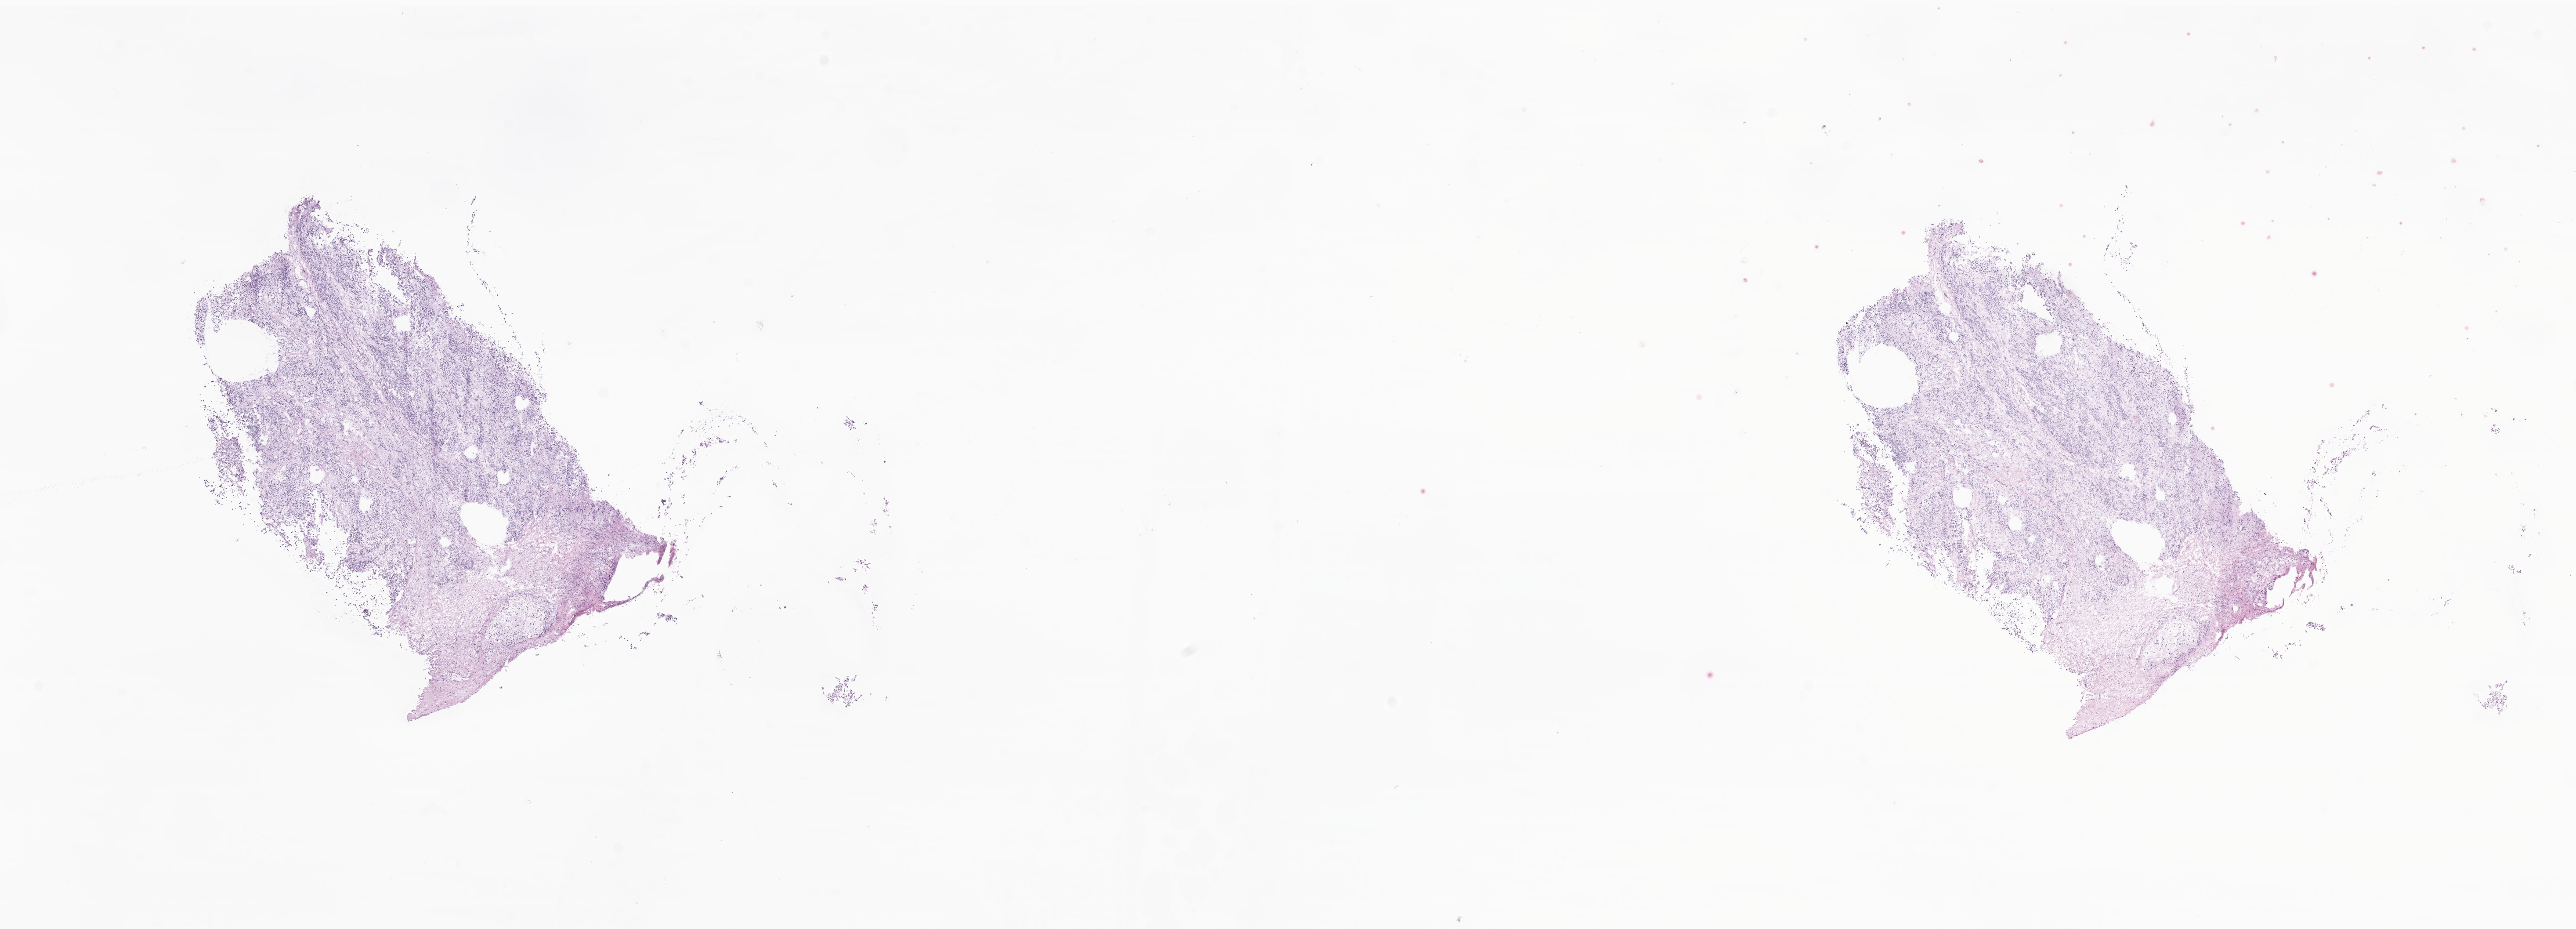
H&E whole-slide image of tumor tissue from the posterior mediastinum — a low-resolution overview of the entire scanned area, about 24.7 x 8.9 mm, frozen section. Male patient, age 114 months (9 years 6 months).
• diagnosis: Neuroblastoma, NOS